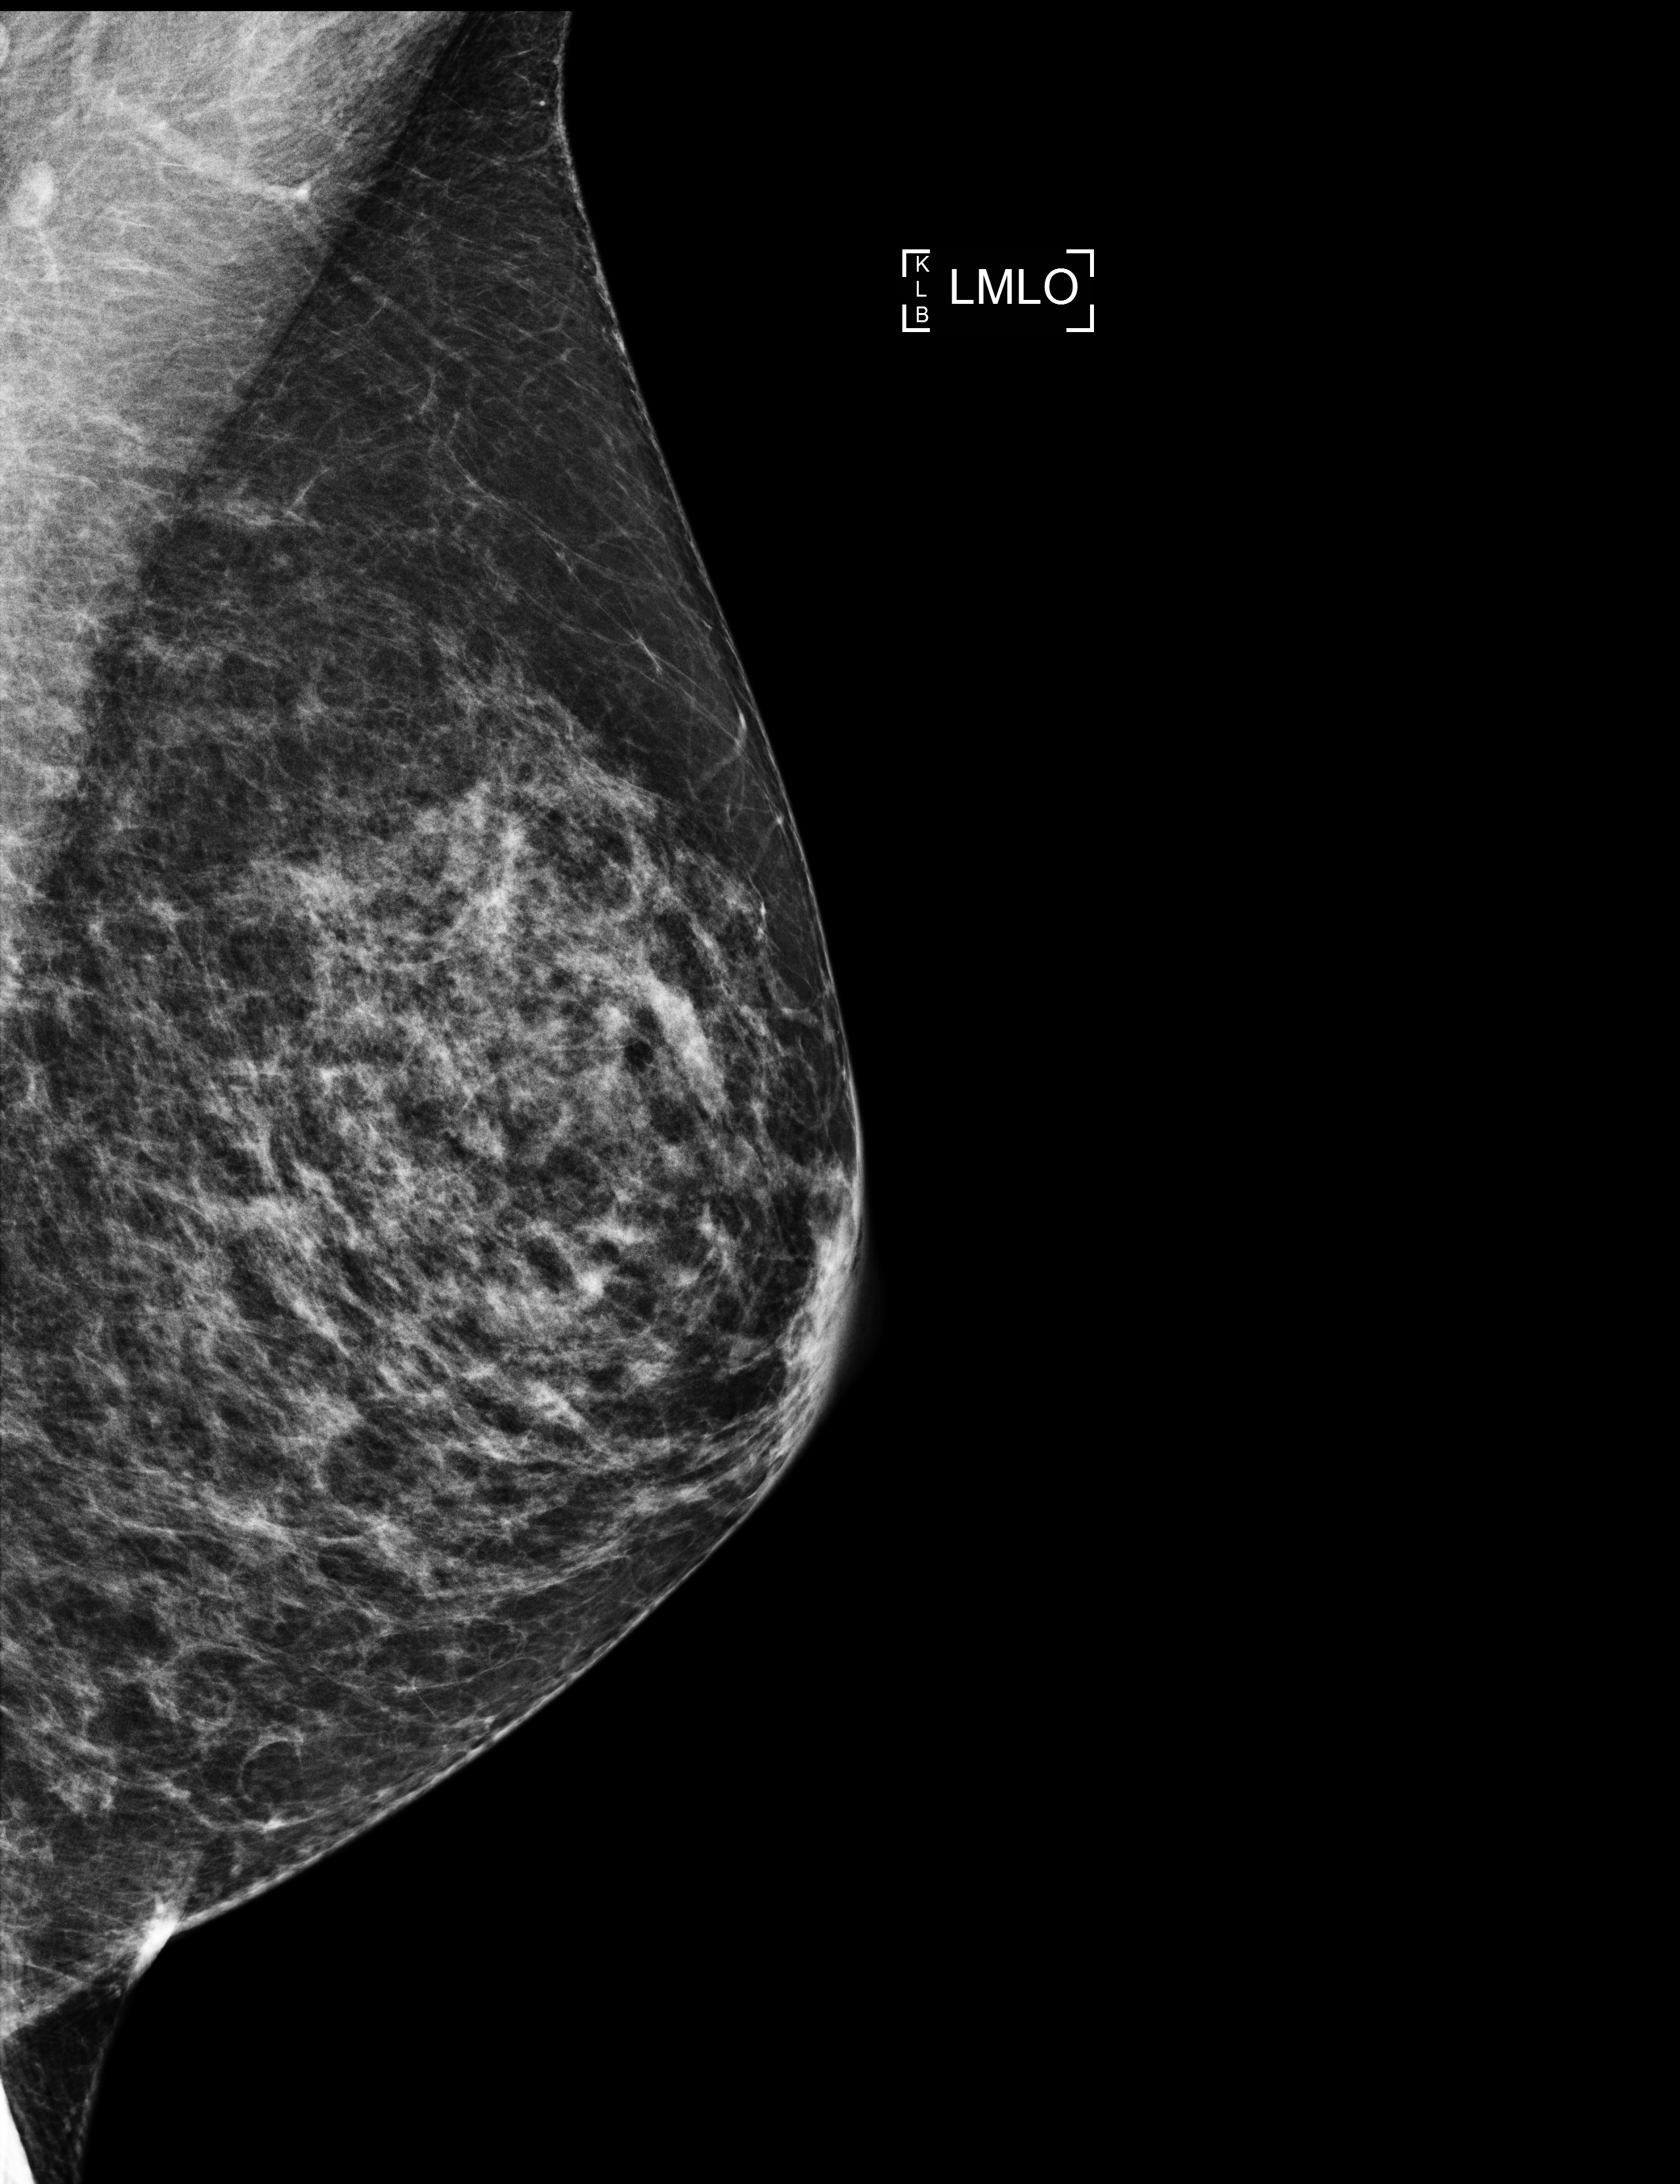
Annual screening mammography examination, compressed breast thickness 55 mm, system: Selenia Dimensions. Female patient, age 64 years.
Image type: full-field digital mammogram. Breast: left. Projection: medio-lateral oblique projection.